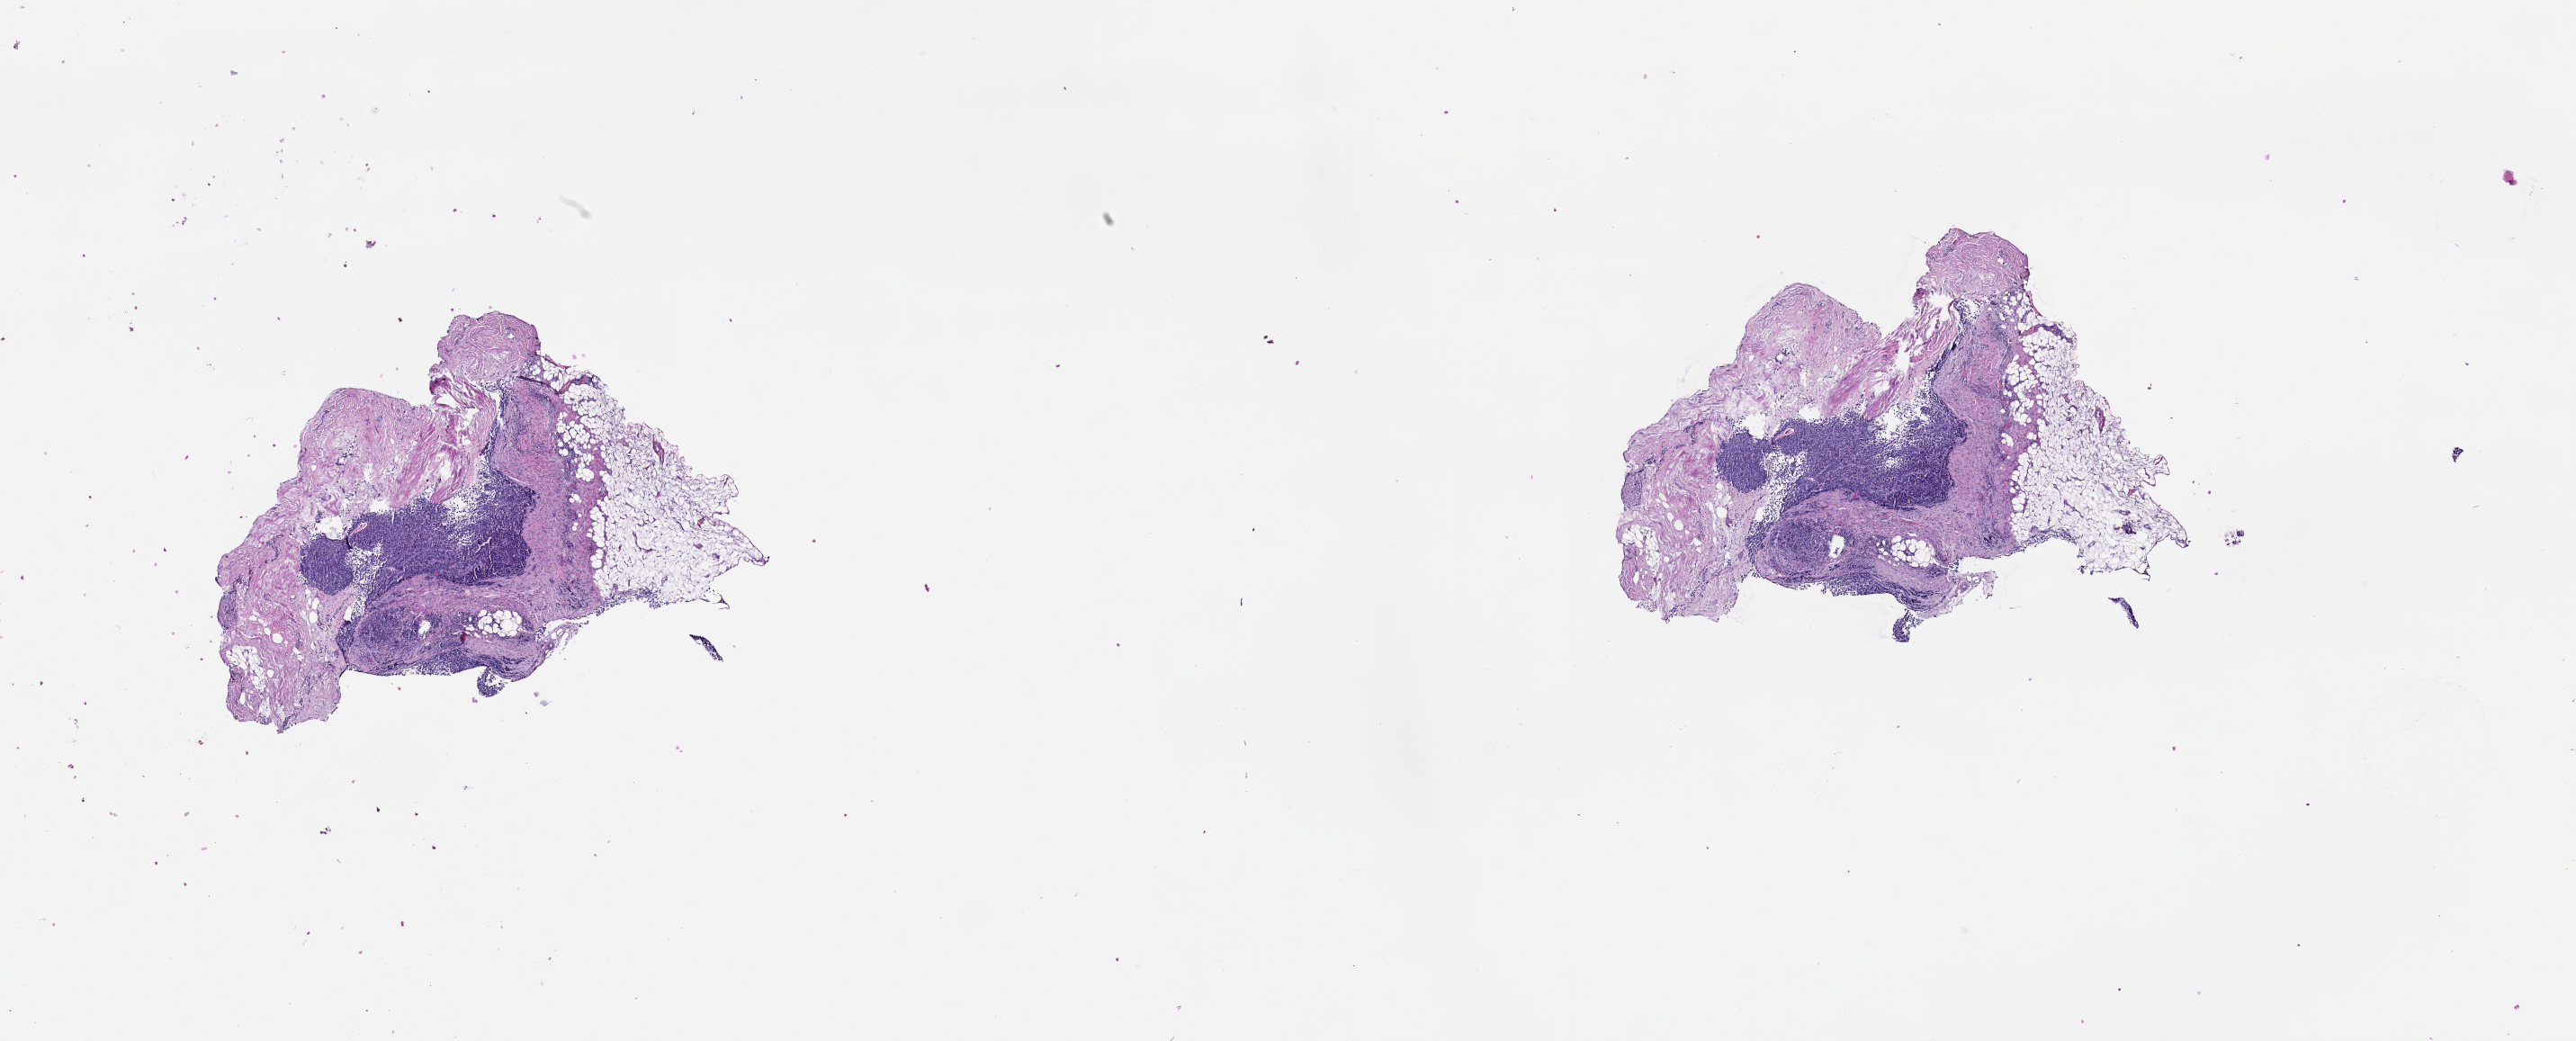
Whole-slide histology image, H&E-stained — shown as a low-resolution overview of the whole scanned area (about 23.1 x 9.3 mm, acquisition: 20x scan). Patient: male, age 53 years.
- patient diagnosis: Malignant melanoma, NOS